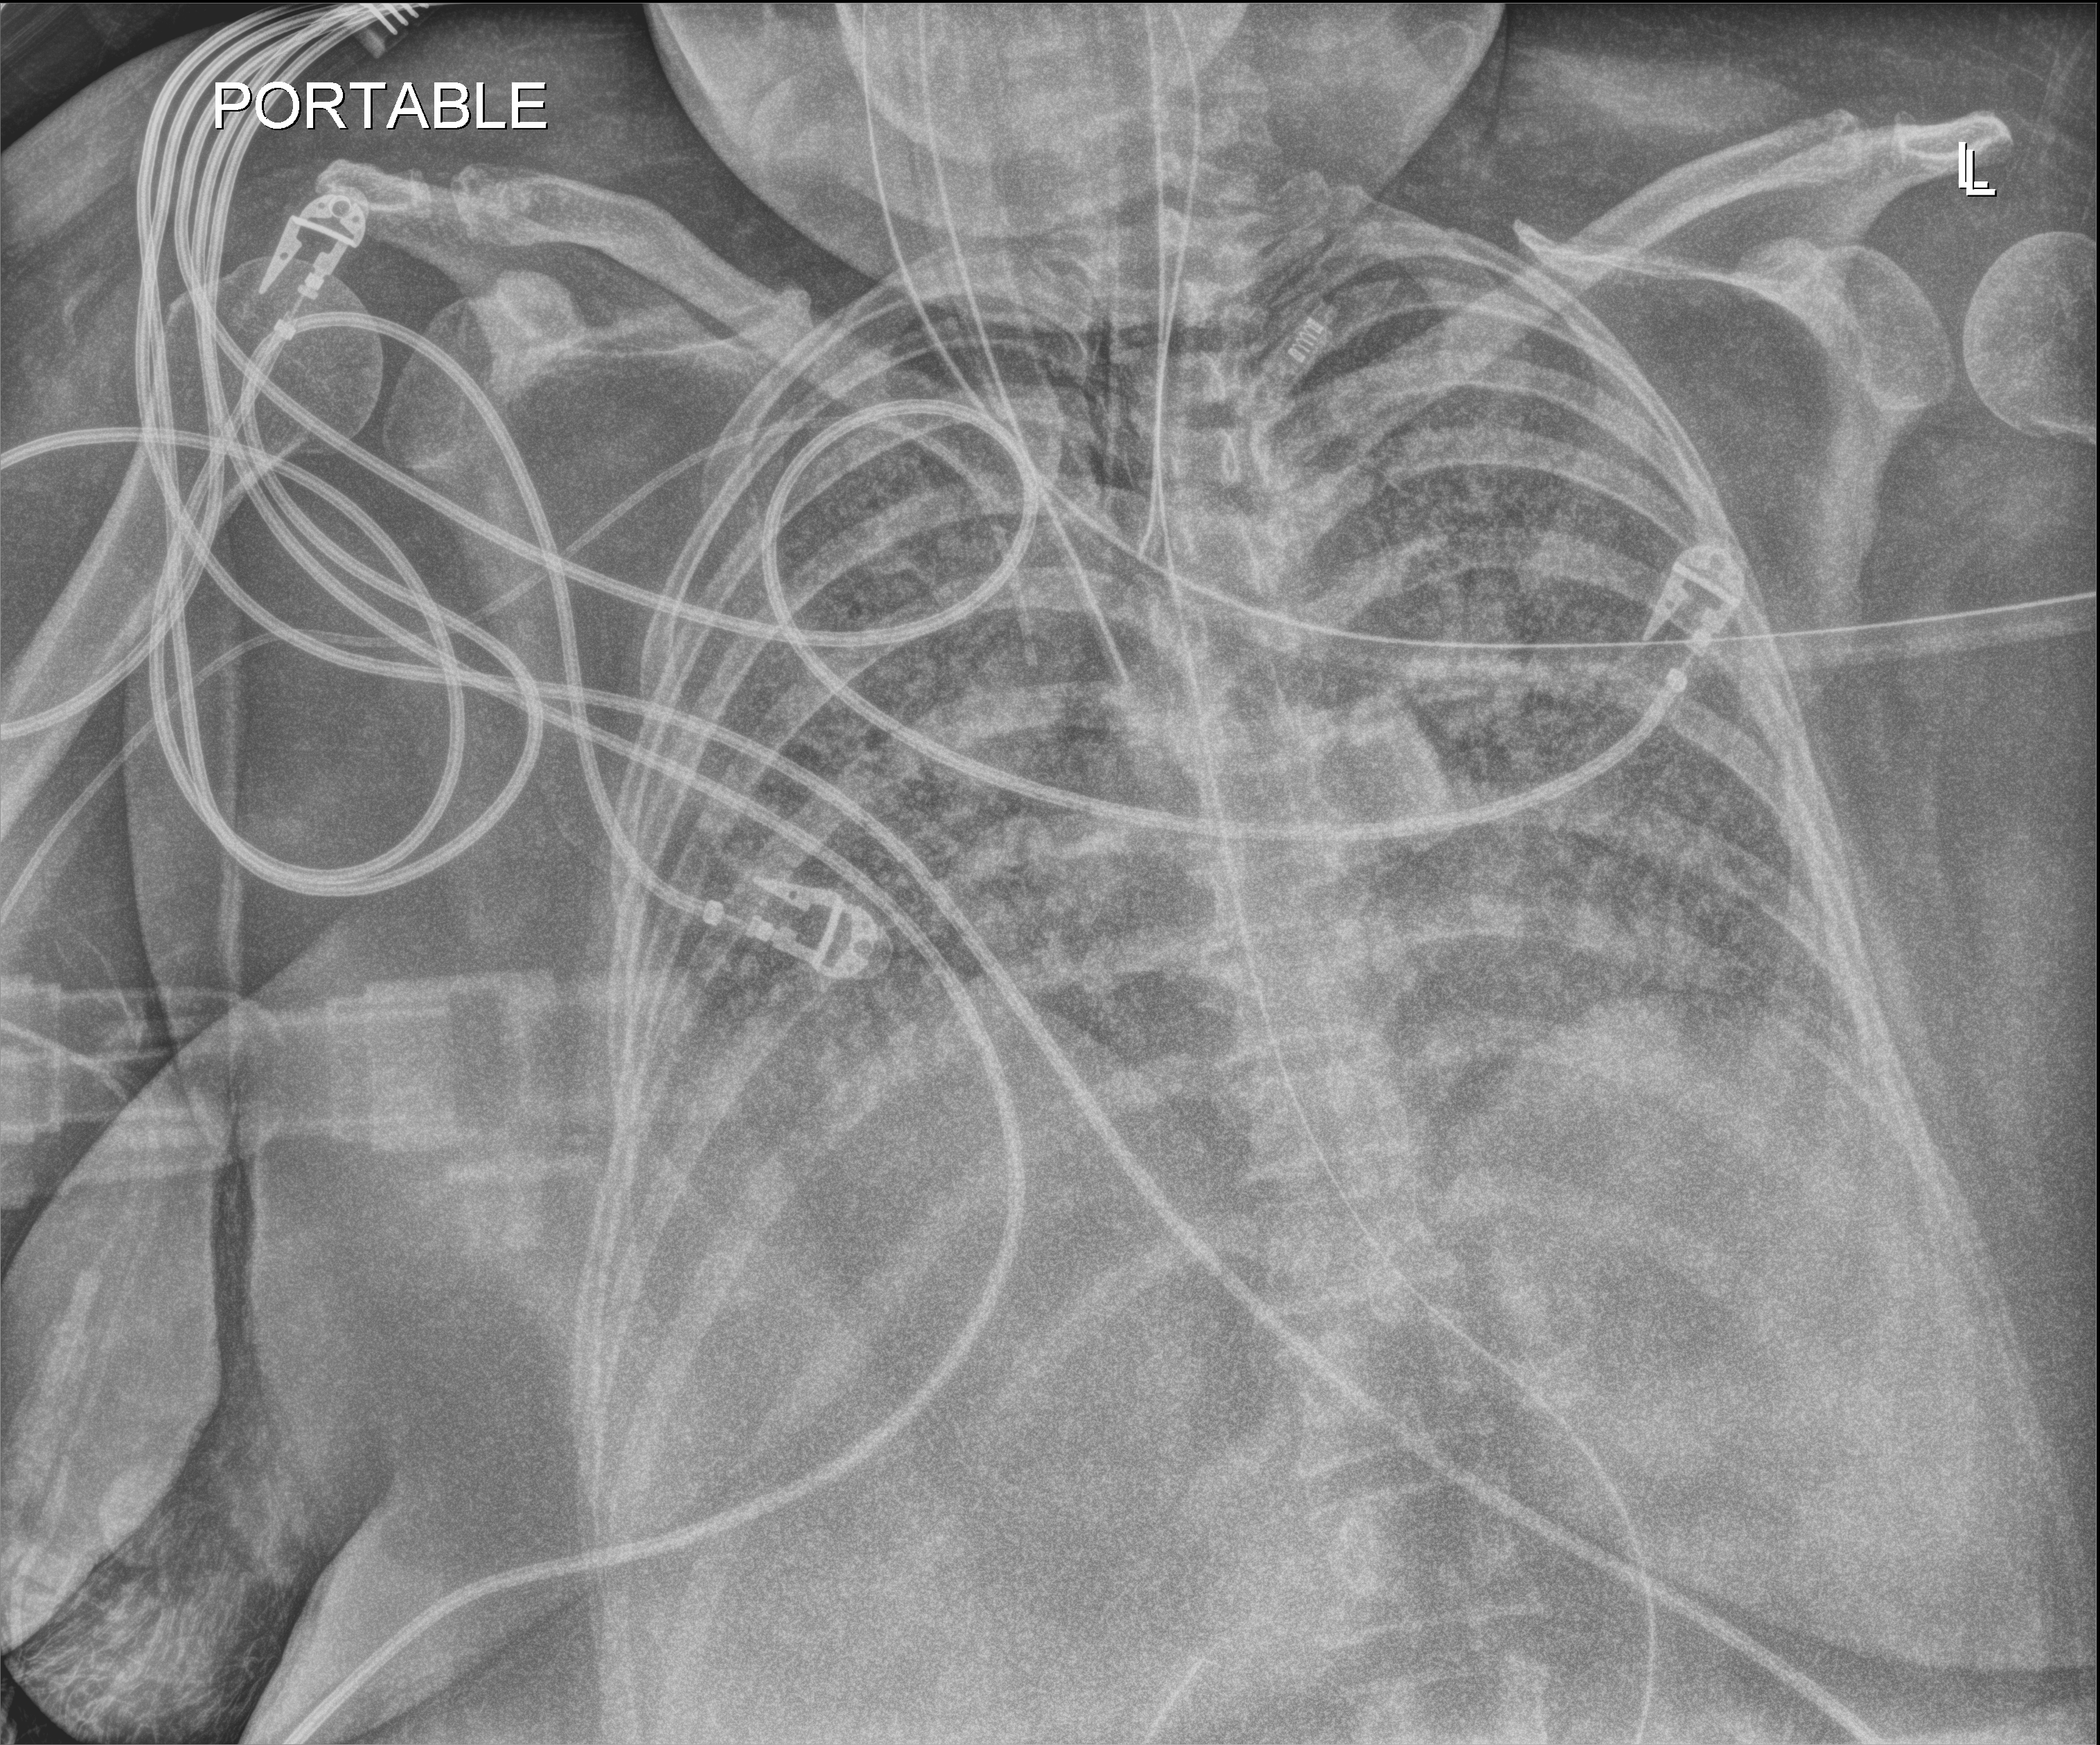
Portable chest radiograph; anteroposterior (AP) projection. Female patient hospitalised with COVID-19, age 18–59 years.
Admission-level facts for this patient (not findings on this image; timing relative to this image not recorded):
- admitted to intensive care during this hospital stay: yes